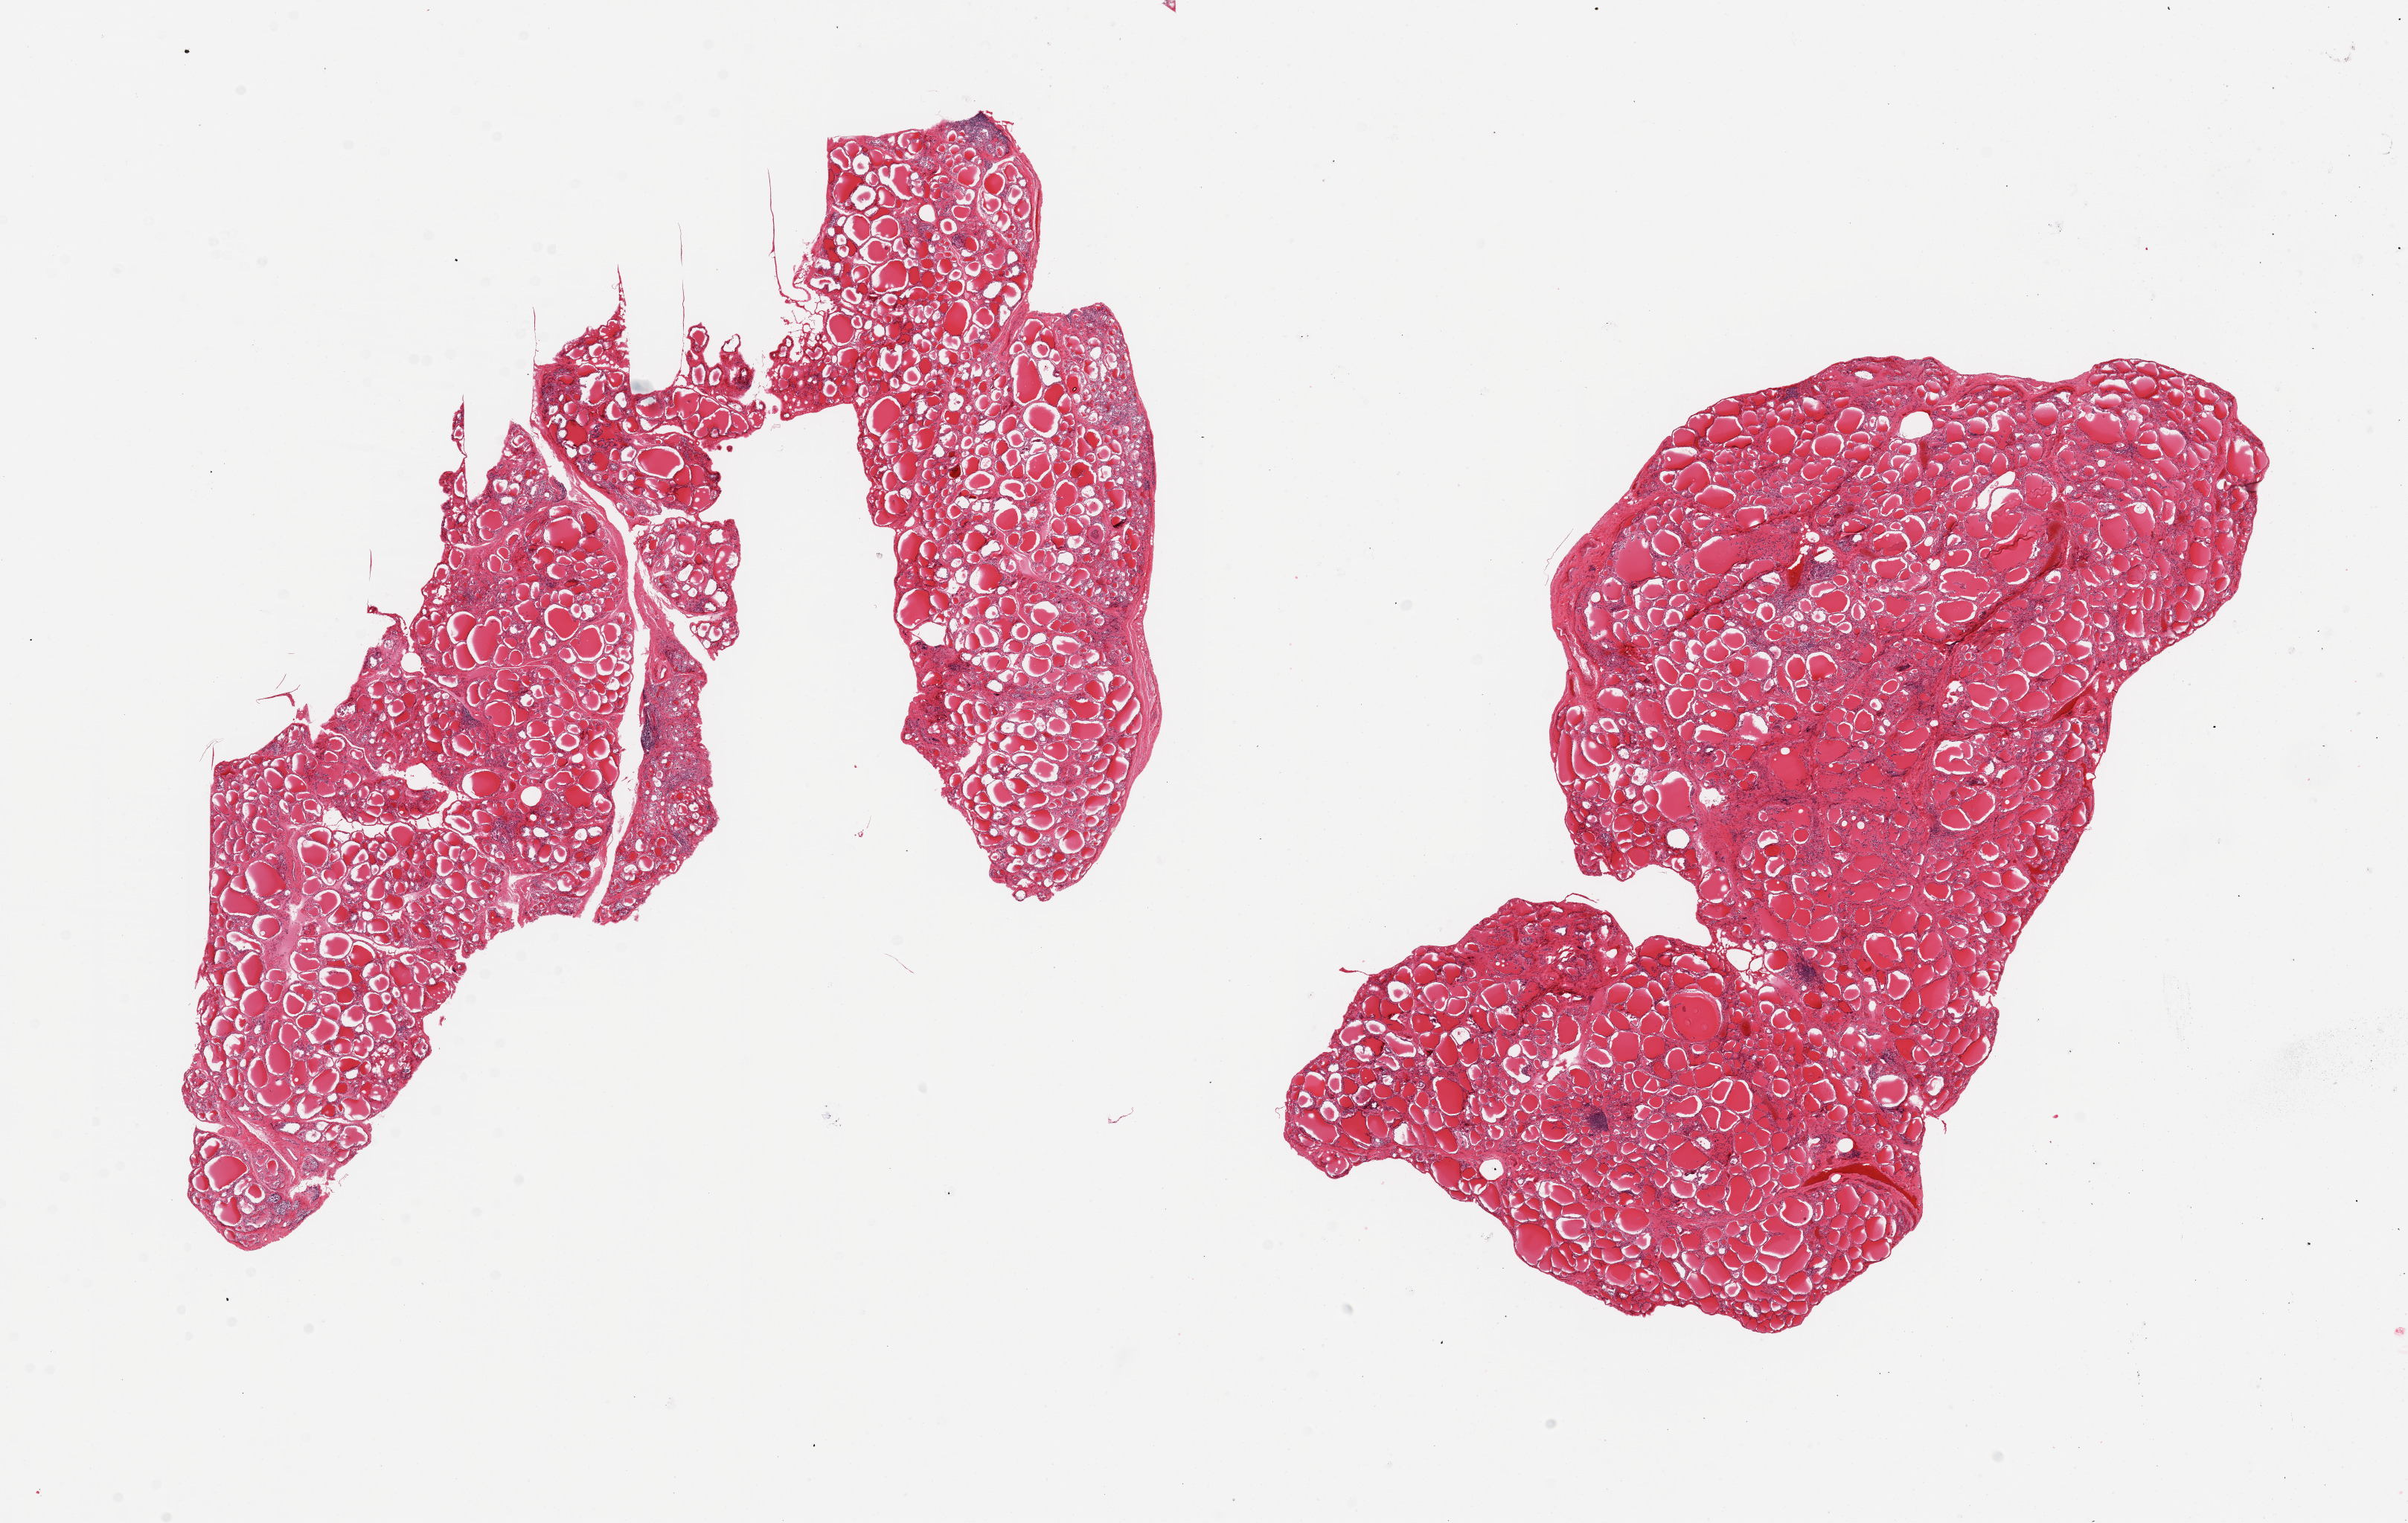
Whole-slide image, hematoxylin and eosin (H&E) stain — low-resolution overview of the scanned area, about 25.6 x 16.2 mm; PAXgene-fixed, paraffin-embedded tissue; sampled site (target tissue): thyroid; tissue donor sample. Donor: male.
Reviewer comment on this tissue sample: 2 pieces, no abnormalities.